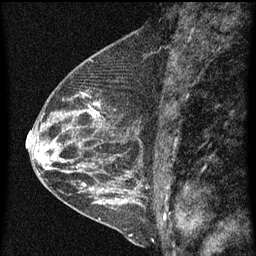
Breast MRI (dynamic contrast-enhanced), one sagittal slice; dynamic contrast-enhanced series, image 2 of 4 at this slice position (ordered by acquisition); 1.5 T; TE 4.2 ms, TR 8 ms; 2 mm slice thickness; 256 × 256 image matrix, field of view 180 × 180 mm. Patient: female, 48 years.
Outlined on this slice (semi-automatic segmentation, software-assisted and operator-edited):
- analysis volume of interest (the breast-tissue region the enhancement analysis was run in; not a lesion): bounding box [x1, y1, x2, y2] px = [73, 86, 108, 139]
- tumour enhancement mask (voxels above the 70 % enhancement threshold inside the analysis volume of interest): [86, 96, 100, 119]